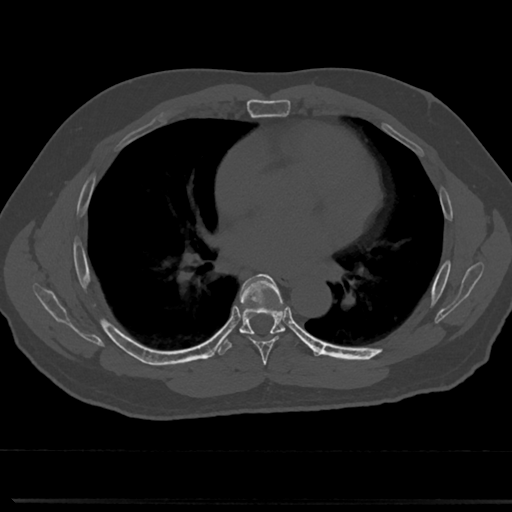
CT including the spine, one axial slice. Reconstruction kernel Br40s/3. 120 kVp. Bone window (W 1800 / L 400 HU). 0.5 mm slice thickness. 512 × 512 image matrix. Patient: male, 61 years. From the clinical record (not read from this slice): primary cancer: prostate.
Outlined on this slice (semi-automatically segmented with operator editing):
- T5 vertebra: bounding box [x1, y1, x2, y2] px = [266, 371, 270, 376]
- T6 vertebra: [239, 275, 289, 358]
- T7 vertebra: [240, 325, 285, 335]